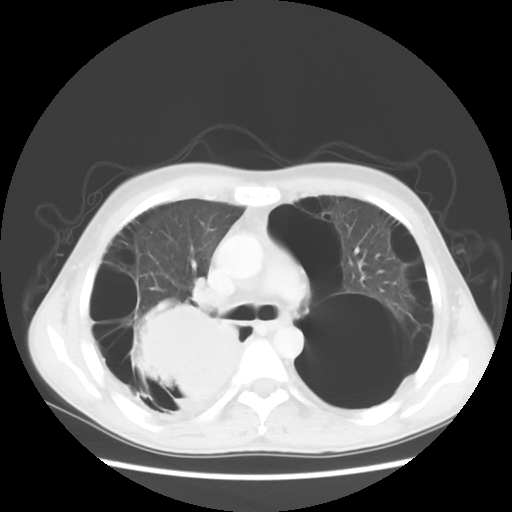
Chest CT, one axial slice; position 35 of 56 along the scan axis; reconstruction kernel STANDARD; 140 kVp; lung window (W 1500 / L -600 HU); 5 mm slice thickness; 512 × 512 image matrix, field of view 351 × 351 mm. Patient: male, 41 years. Case-level facts recorded for this patient, not image findings: clinical TNM (as recorded): T4 N0 M1a; histopathological grade: G3.
Outlined on this slice (rectangle marked by the reading radiologist):
- lung tumour (recorded histology: large cell carcinoma): bounding box [x1, y1, x2, y2] px = [133, 305, 254, 417]